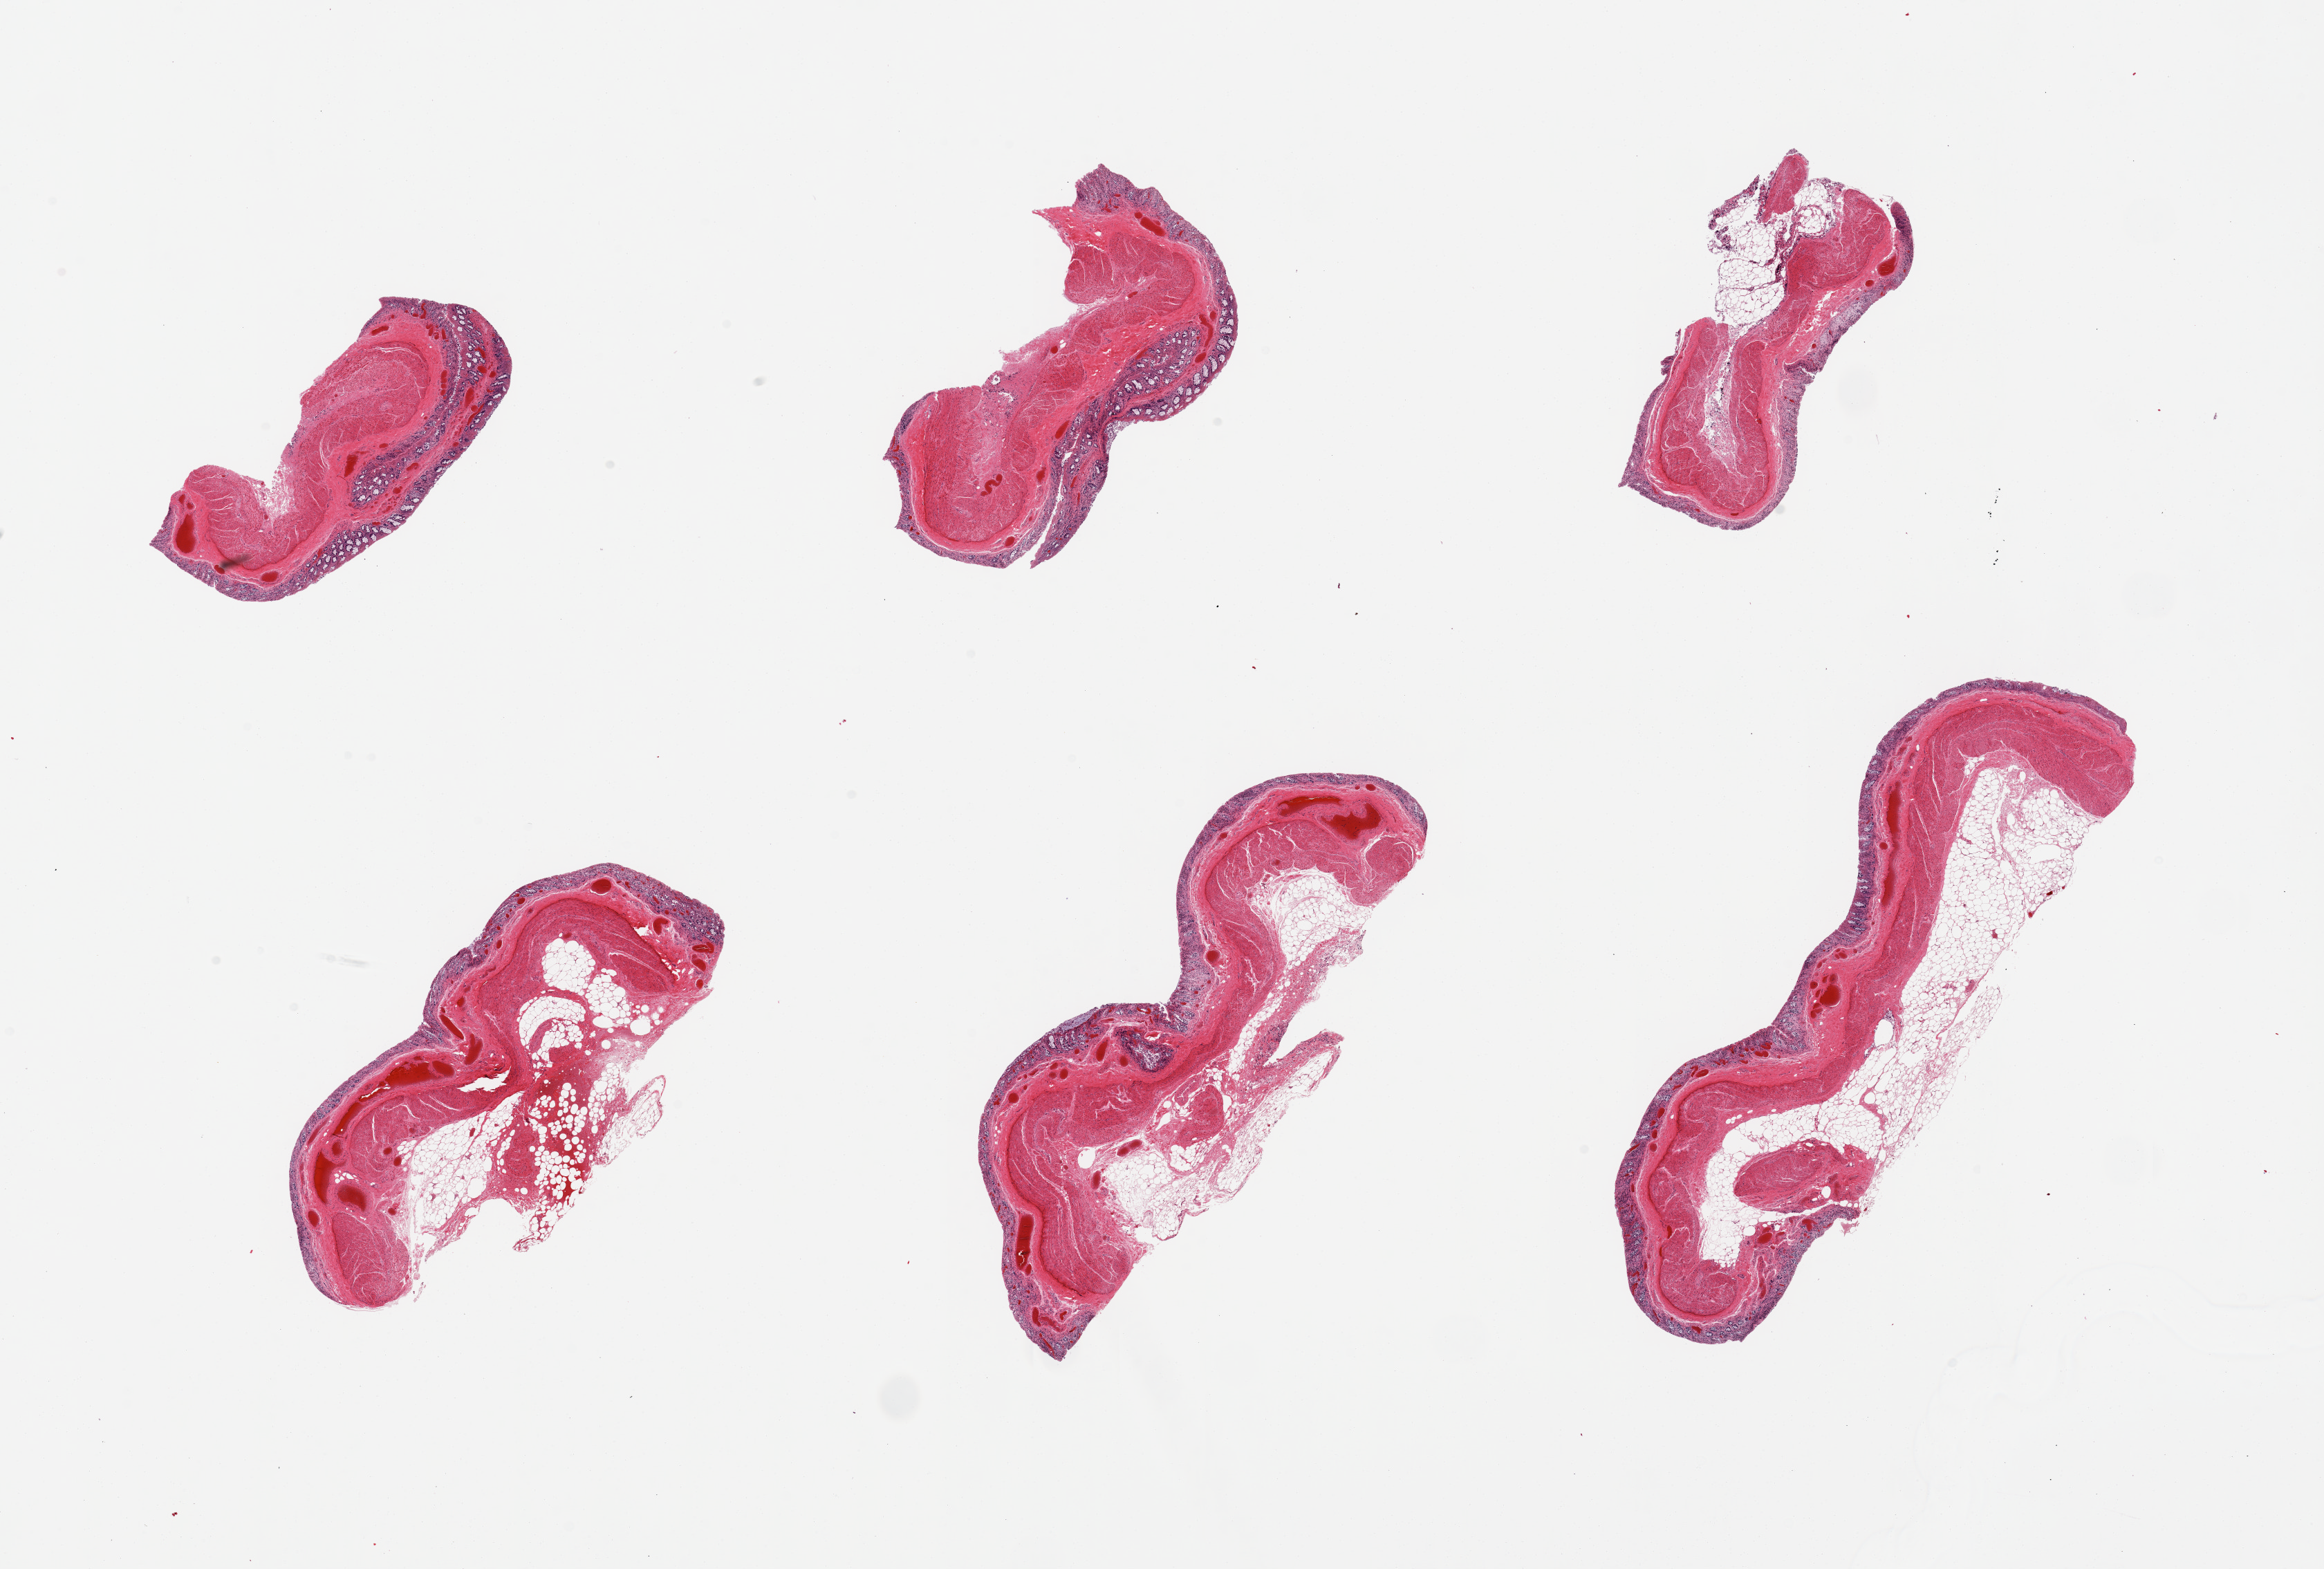
Haematoxylin and eosin whole-slide image, brightfield — shown as a low-resolution overview of the whole scanned area (about 26.6 x 17.9 mm, from a 20x scan). PAXgene-fixed, paraffin-embedded tissue. Section of transverse colon (target tissue). Donor tissue sample. Donor sex: male.
• pathologist's review note for this sample: 6 pieces; 4 of 6 pieces contain 20% to 30% of external fat ;mucosal autolysis grade 2 to 3; muscularis grade 1